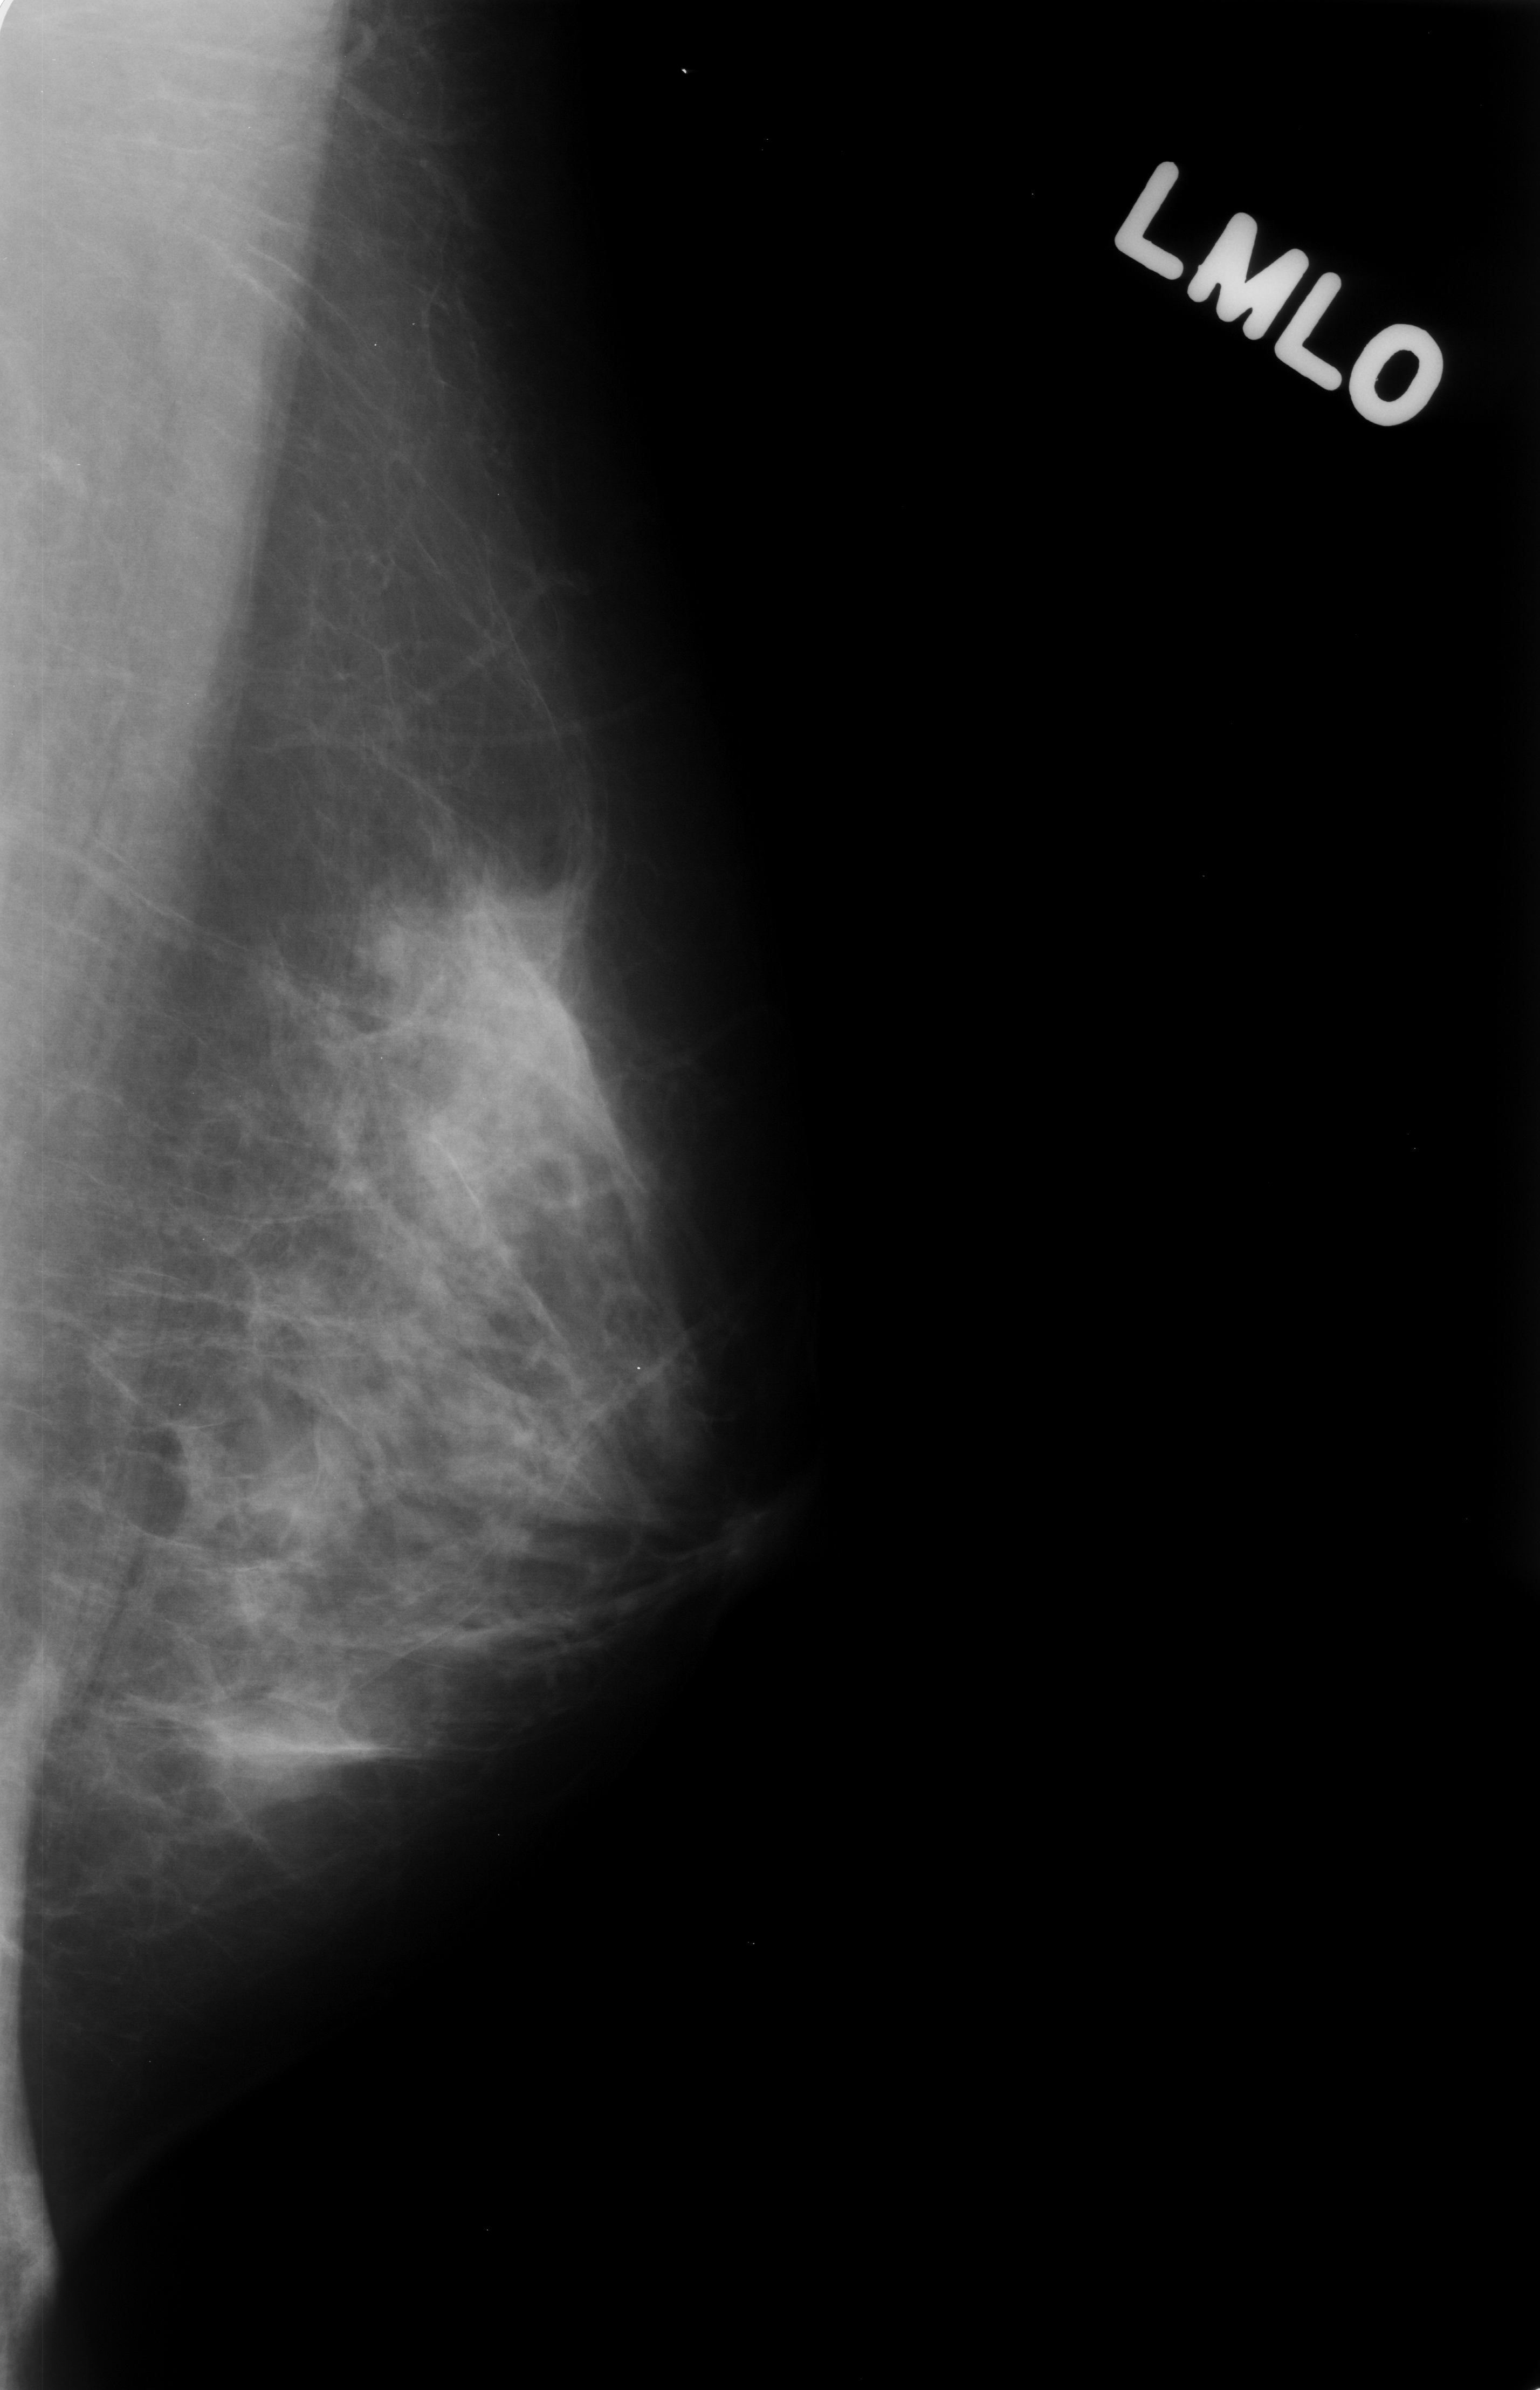
Mammogram (digitized film), left breast, MLO view.
Marked abnormality: mass, shape oval, margins ill defined; BI-RADS assessment category 4; pathology result (as recorded, not read from the image): benign.